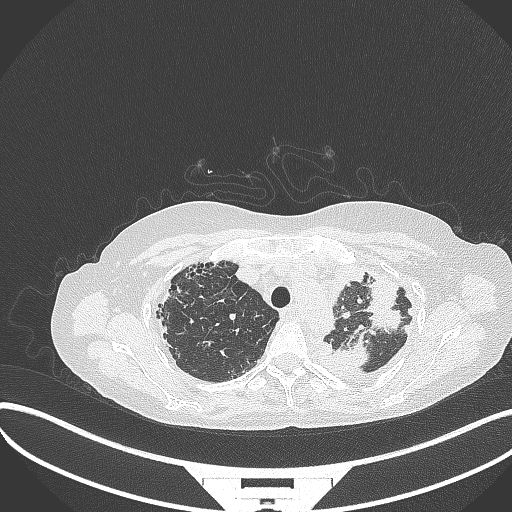
Chest CT, one axial slice. Slice 272 of 373 in the series (ordered by position). Reconstruction kernel B70f. Lung window (W 1500 / L -600 HU). 1 mm slice thickness. 512 × 512 image matrix, field of view 400 × 400 mm. Female patient, age 56 years. Case-level facts recorded for this patient, not image findings: clinical TNM (as recorded): T1 N0 M0.
Annotated regions visible in this slice (rectangle marked by the reading radiologist):
- lung tumour (recorded histology: adenocarcinoma): bounding box (x1, y1, x2, y2) in pixels: (337, 339, 372, 369)
- lung tumour (recorded histology: adenocarcinoma): (359, 275, 410, 331)